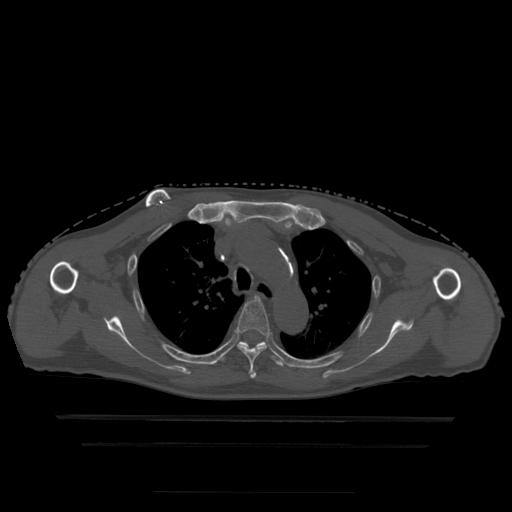
CT including the spine, one axial slice. Position 350 of 522 along the scan axis. Bone window (W 1800 / L 400 HU). 1.25 mm slice thickness. 512 × 512 image matrix, field of view 436 × 436 mm. Patient age 68 years. Case-level facts recorded for this patient, not image findings: primary cancer: urothelial.
Outlined on this slice (semi-automatically segmented with operator editing):
- T4 vertebra: box from (x=236, y=298) to (x=271, y=379) px
- T5 vertebra: (x=221, y=342)–(x=284, y=368)